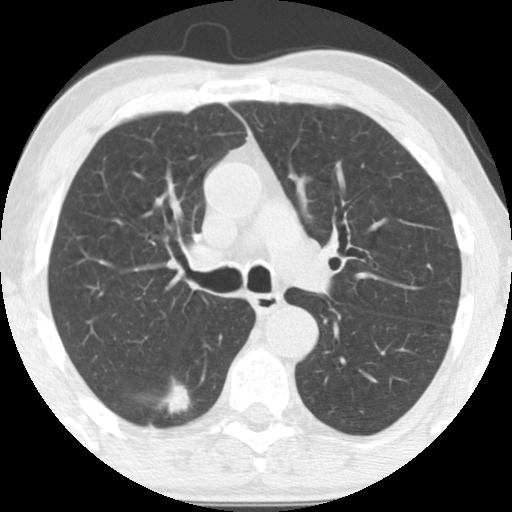
Low-dose screening chest CT, one axial slice. Reconstruction kernel STANDARD. Lung window (W 1500 / L -600 HU). 2.5 mm slice thickness. 512 × 512 image matrix, field of view 300 × 300 mm.
Structures marked on this image (expert manual segmentation):
- lesion 1 (tumor, lower lobe of right lung): box from (x=162, y=381) to (x=190, y=414) px